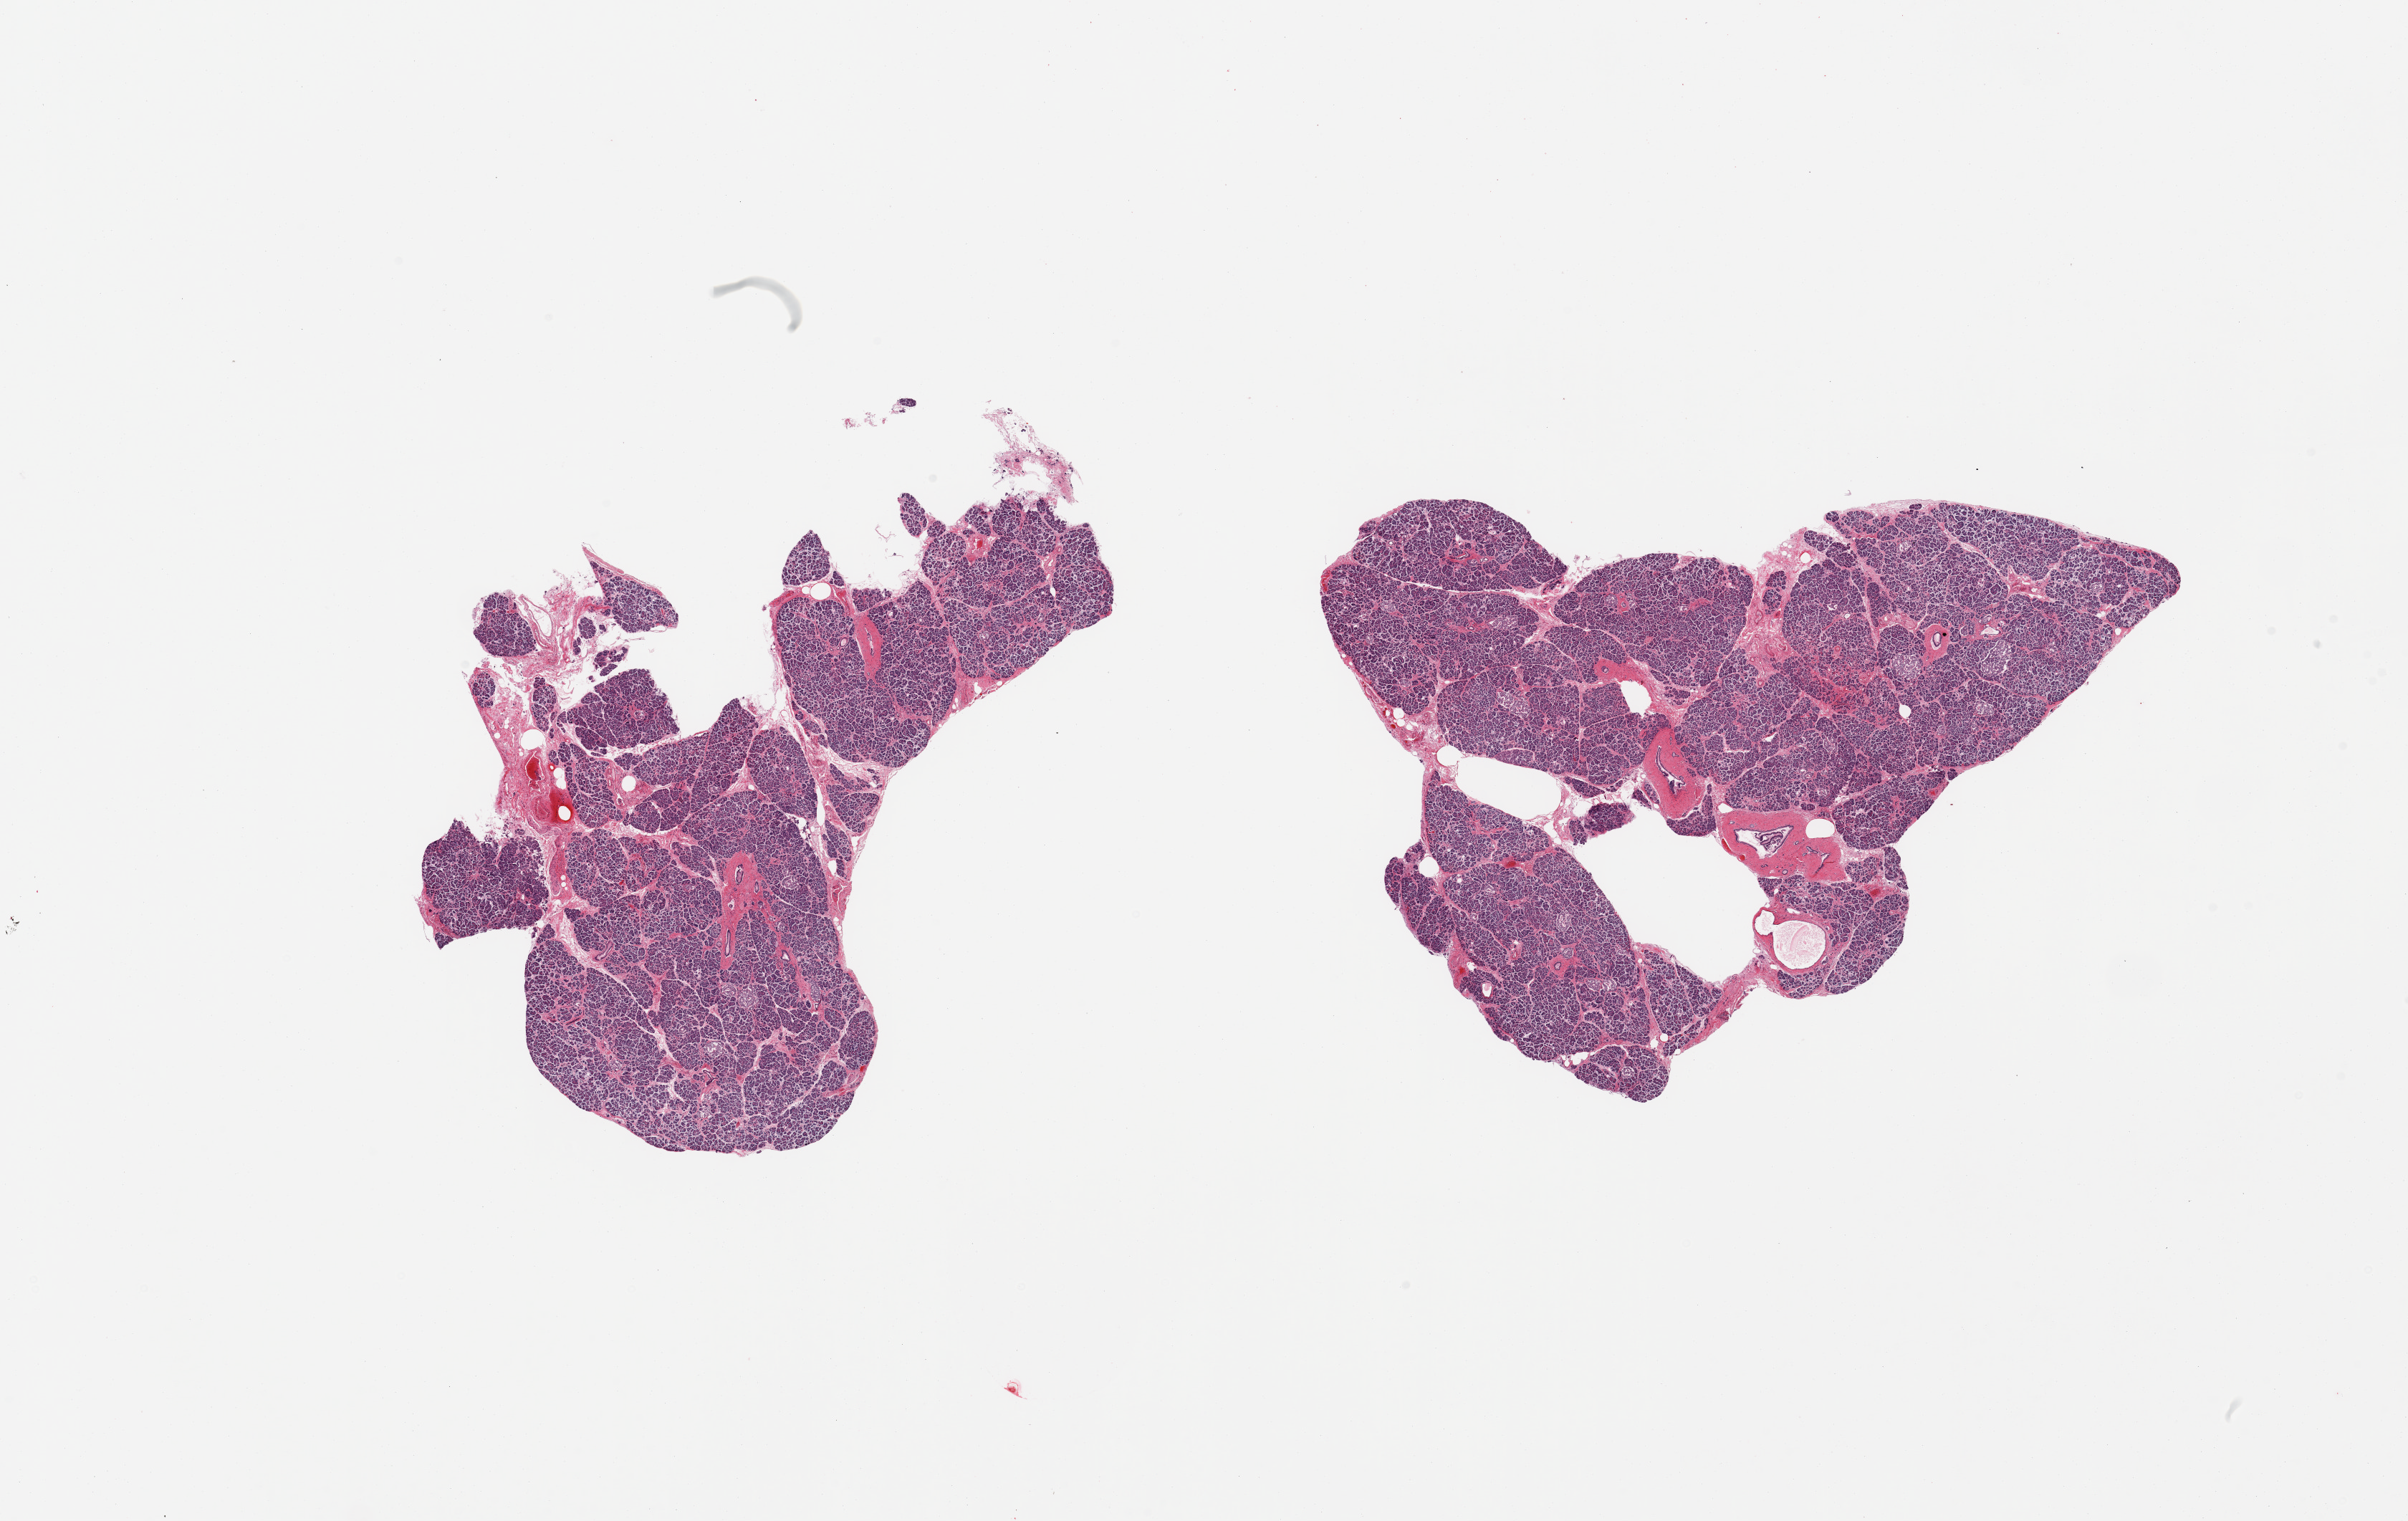
Haematoxylin and eosin whole-slide image — a low-resolution overview of the entire scanned area, about 26.6 x 16.8 mm. PAXgene-fixed, paraffin-embedded tissue. Target tissue: pancreas. Tissue donor sample.
Reviewer comment on this tissue sample: 2 pieces; well trimmed.